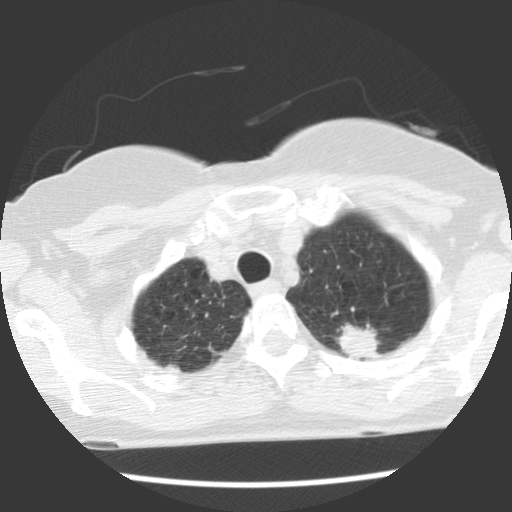
Low-dose screening chest CT, one axial slice. Position 100 of 120 along the scan axis. Reconstruction kernel STANDARD. Lung window (W 1500 / L -600 HU). 2.5 mm slice thickness. 512 × 512 image matrix, field of view 300 × 300 mm.
Structures marked on this image (outlined manually by an expert reader):
- lesion 1 (tumor, upper lobe of left lung): bounding box <336,323,380,360> (left, top, right, bottom; pixels)